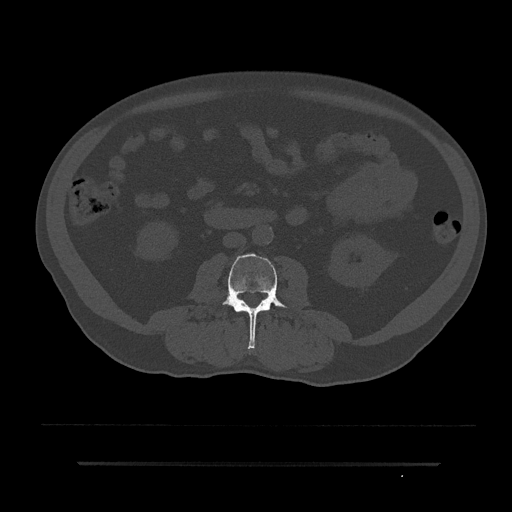
CT including the spine, one axial slice; position 4 of 797 along the scan axis; 120 kVp; bone window (W 1800 / L 400 HU); 0.5 mm slice thickness; 512 × 512 image matrix, field of view 464 × 464 mm. Male patient, age 59 years. From the clinical record (not read from this slice): primary cancer: bile ducts; vertebrae with lytic lesions (as recorded): T10.
Outlined on this slice (semi-automatic segmentation, software-assisted and operator-edited):
- L3 vertebra: box from (x=215, y=253) to (x=289, y=349) px